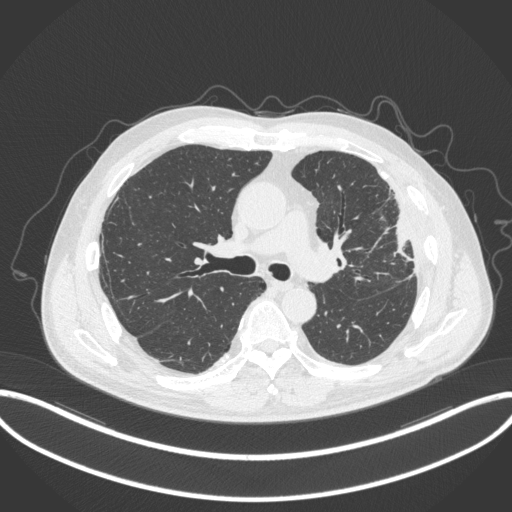
Chest CT, one axial slice; position 211 of 382 along the scan axis; lung window (W 1500 / L -600 HU); 512 × 512 image matrix, field of view 415 × 415 mm. Patient: male, 64 years. From the clinical record (not read from this slice): clinical TNM (as recorded): T4 N1 M0; histopathological grade: G3.
Structures marked on this image (bounding box drawn by a radiologist):
- lung tumour (recorded histology: adenocarcinoma): bounding box <387,212,415,264> (left, top, right, bottom; pixels)